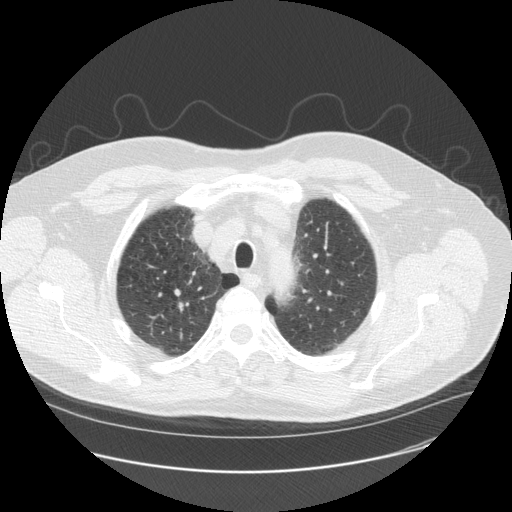
Axial slice from a low-dose chest CT screening exam, second annual screen, lung window (W 1500 / L -600 HU), 2.5 mm slice thickness, standard (soft-tissue) reconstruction kernel (STANDARD), 120 kVp. Male, age 61 years at enrolment.
- Expert-annotated lung lesion, bounding box (x1, y1, x2, y2) in pixels: (162, 290, 200, 326).
- Screening reader's record for this exam: no non-calcified nodule ≥4 mm recorded.
- Participant outcome: lung cancer diagnosed 467 days after this screen (after the third annual screen) — squamous cell carcinoma, NOS, right upper lobe, moderately differentiated (G2), stage IA (AJCC 6th edition), 10 mm at pathology.